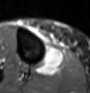
MRI of an extremity soft-tissue mass, one axial slice; position 31 of 60 along the scan axis; STIR; MR volume resampled by the dataset authors to the PET/CT grid (not the native acquisition matrix); 90 × 93 image matrix, field of view 88 × 91 mm. Female patient. From the clinical record (not read from this slice): histological type: undifferentiated – high grade; grade: high; site of the primary tumour: right thigh.
Structures marked on this image (expert contour drawn on MRI and transferred to this co-registered scan by the dataset authors):
- gross tumour volume (mass): box from (x=35, y=40) to (x=66, y=77) px